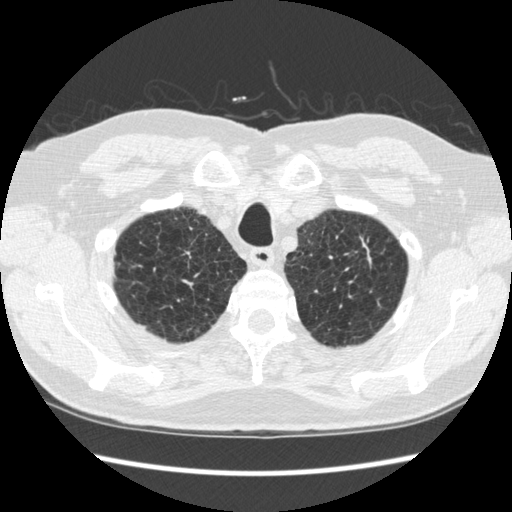
Low-dose screening chest CT, axial slice; second screening round (one year after baseline); lung window (W 1500 / L -600 HU); slice 42 of 295 in the series; 512 × 512 image matrix. Male participant, aged 70 years at enrolment. Former smoker at enrolment.
Lesion marked by an expert reader, bounding box [x1, y1, x2, y2] px = [329, 223, 391, 291]. The screening reader recorded 5 non-calcified nodules or masses ≥4 mm on this exam; which of them this box marks is not recorded. Lung cancer was diagnosed 479 days after this screen (after the third annual screen): squamous cell carcinoma, NOS, left upper lobe, moderately differentiated (G2), stage IA (AJCC 6th edition), 18 mm at pathology.